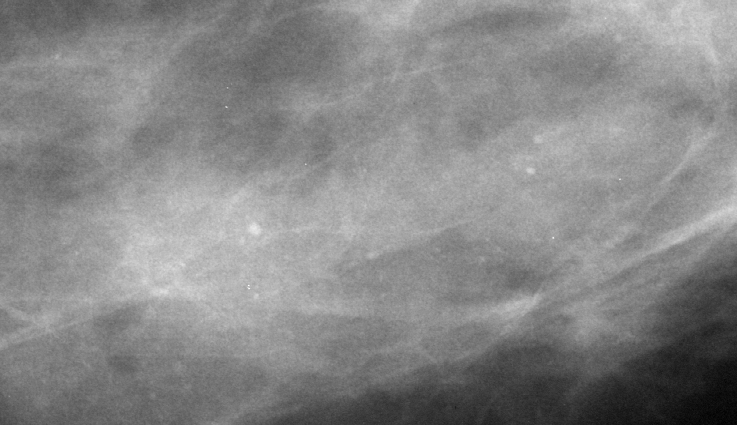
Crop from a digitized film mammogram around one marked abnormality; left breast; CC view; BI-RADS breast density category 2 (scale 1–4).
- Finding: calcifications, morphology amorphous, distribution segmental; BI-RADS assessment category 4; pathology (as recorded): benign.